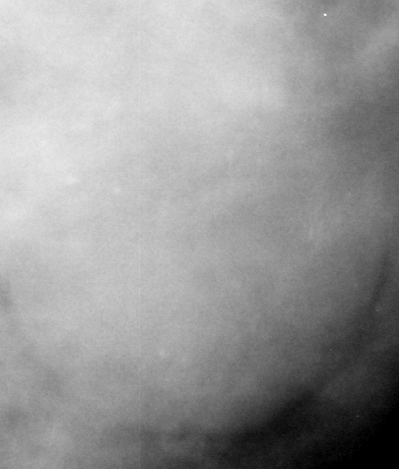
Cropped region of a digitized screen-film mammogram centred on a radiologist-marked abnormality; left breast; MLO view.
- Marked abnormality: mass, shape round, margins circumscribed; BI-RADS assessment category 3; pathology result (as recorded, not read from the image): benign.